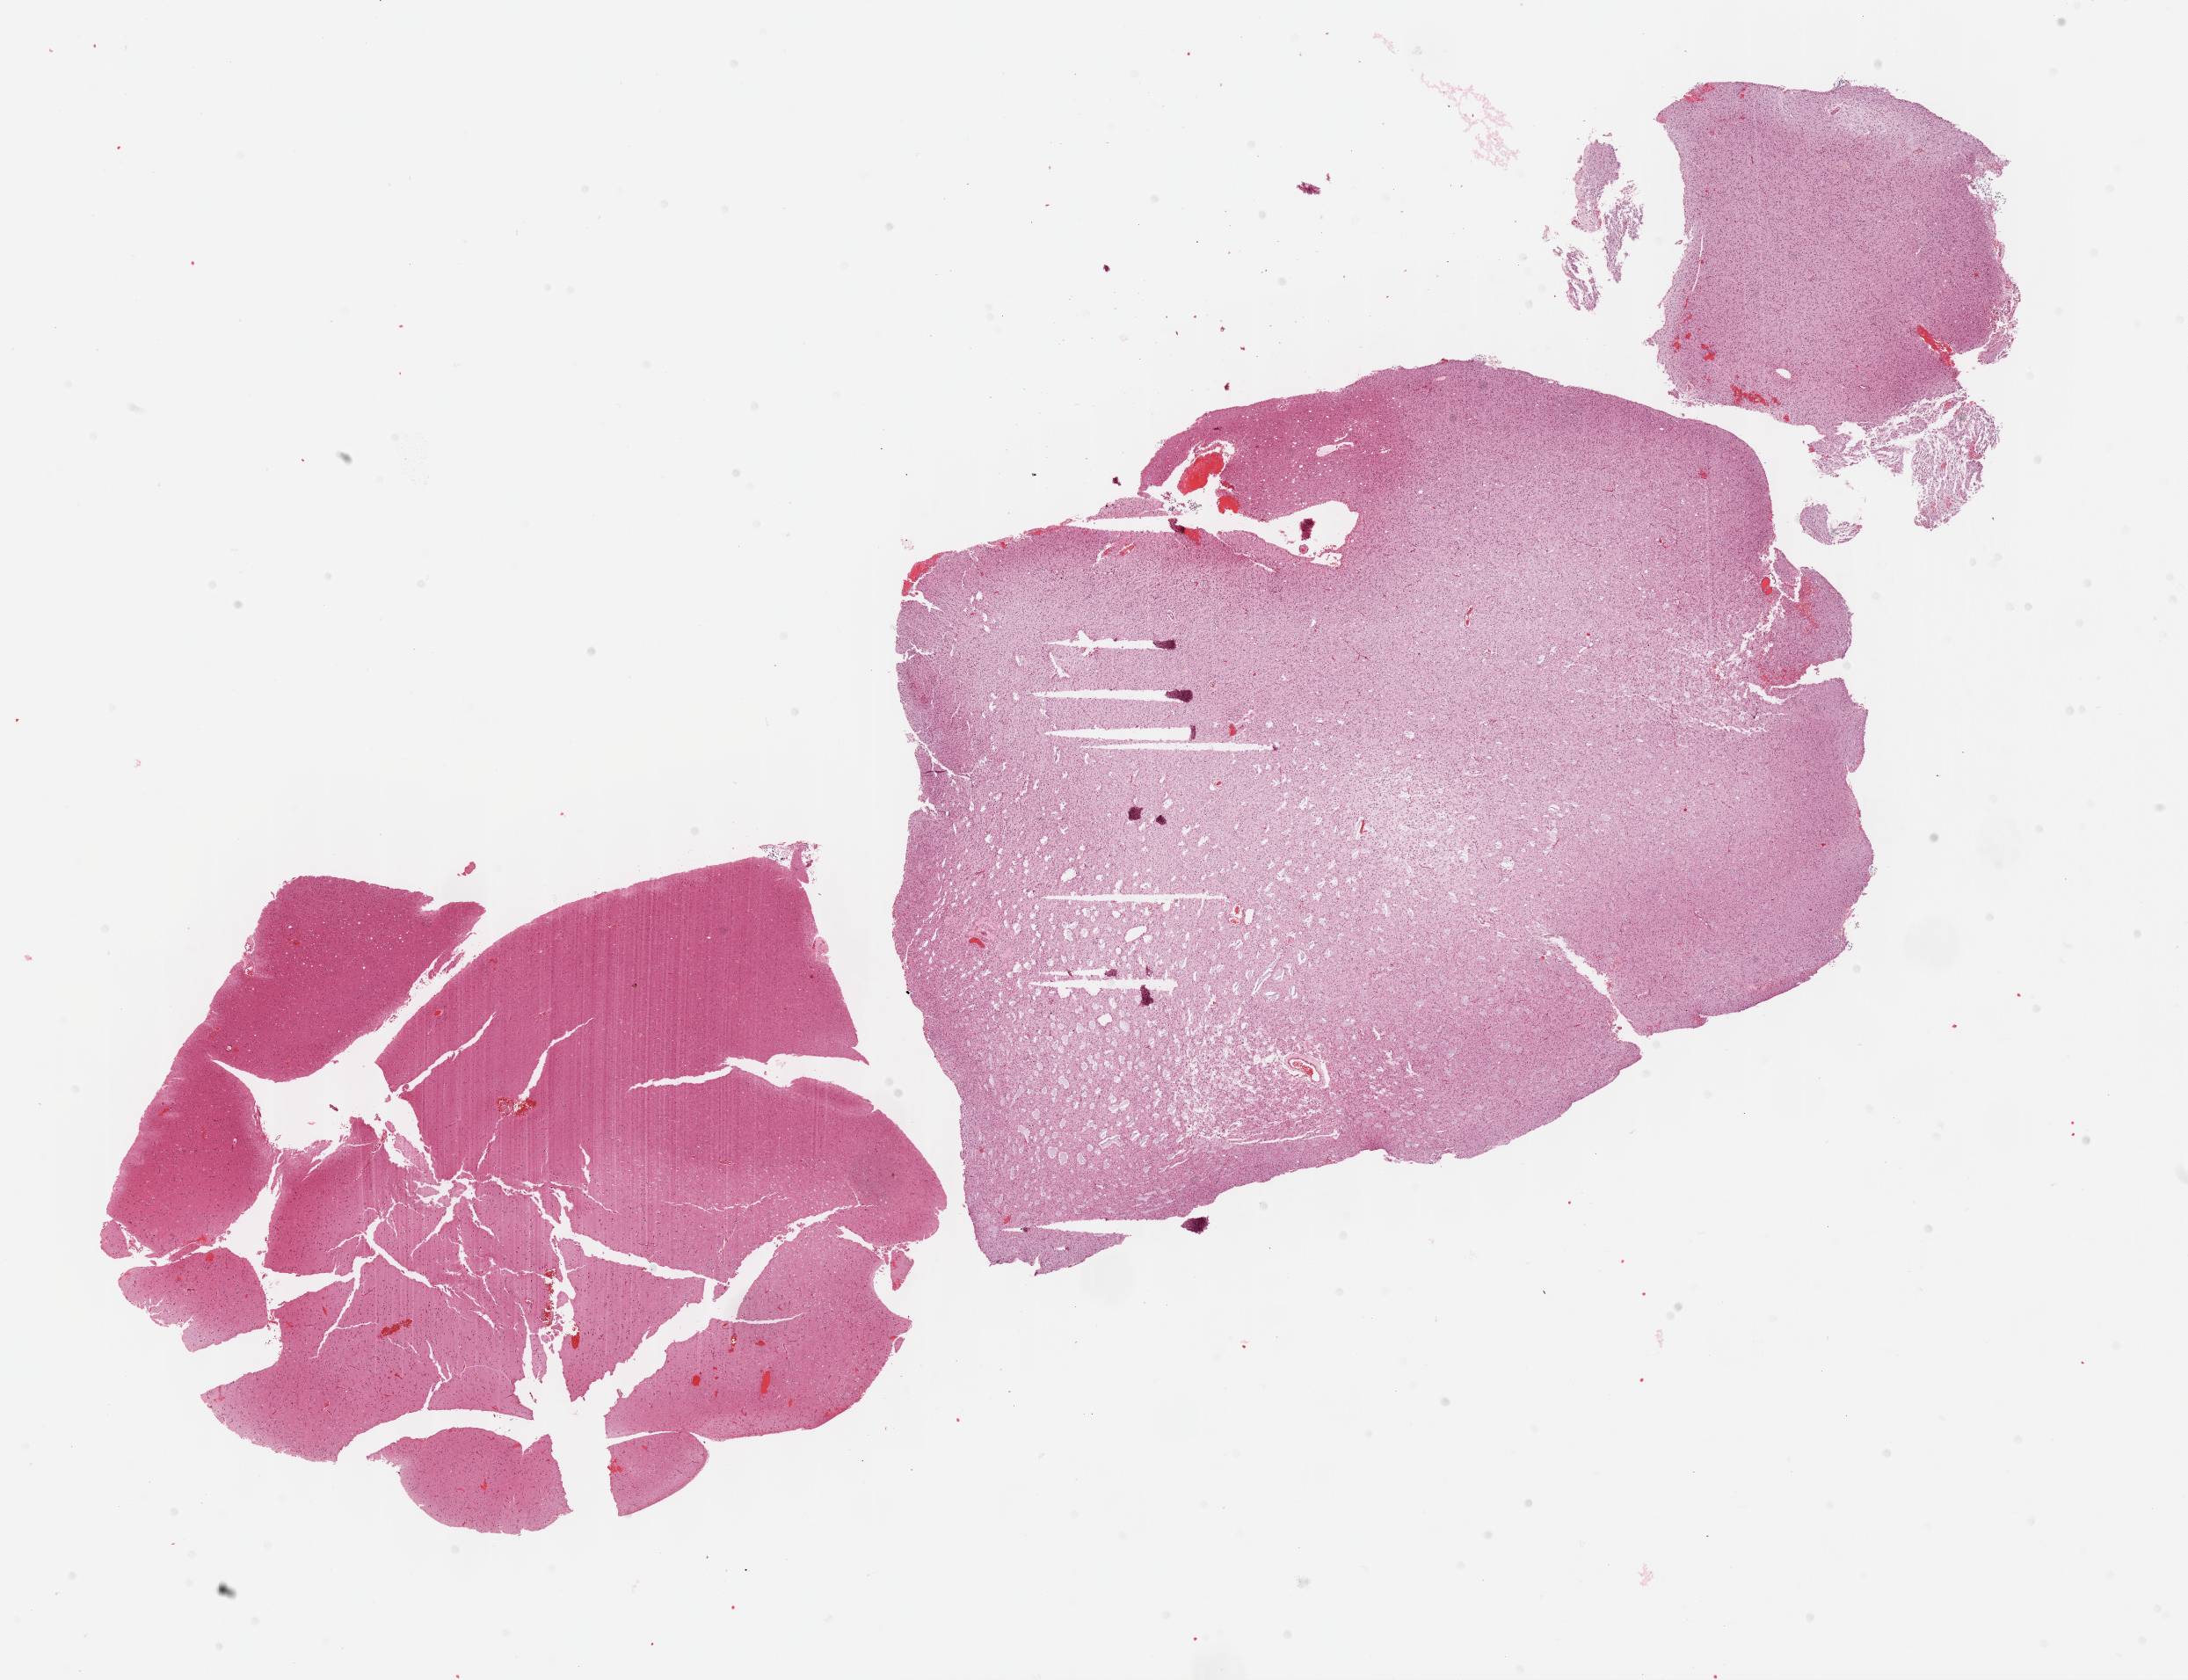
Whole-slide histology image, H&E-stained — whole scanned area (about 20.1 x 15.5 mm, slide scanned at 40x) shown as a low-resolution overview. Formalin-fixed paraffin-embedded (FFPE) diagnostic section. Primary tumour sample from the brain. Female patient; age at initial diagnosis 40 years. Histologic grade: G2 (moderately differentiated).
Histologic diagnosis: Mixed glioma (cerebrum).